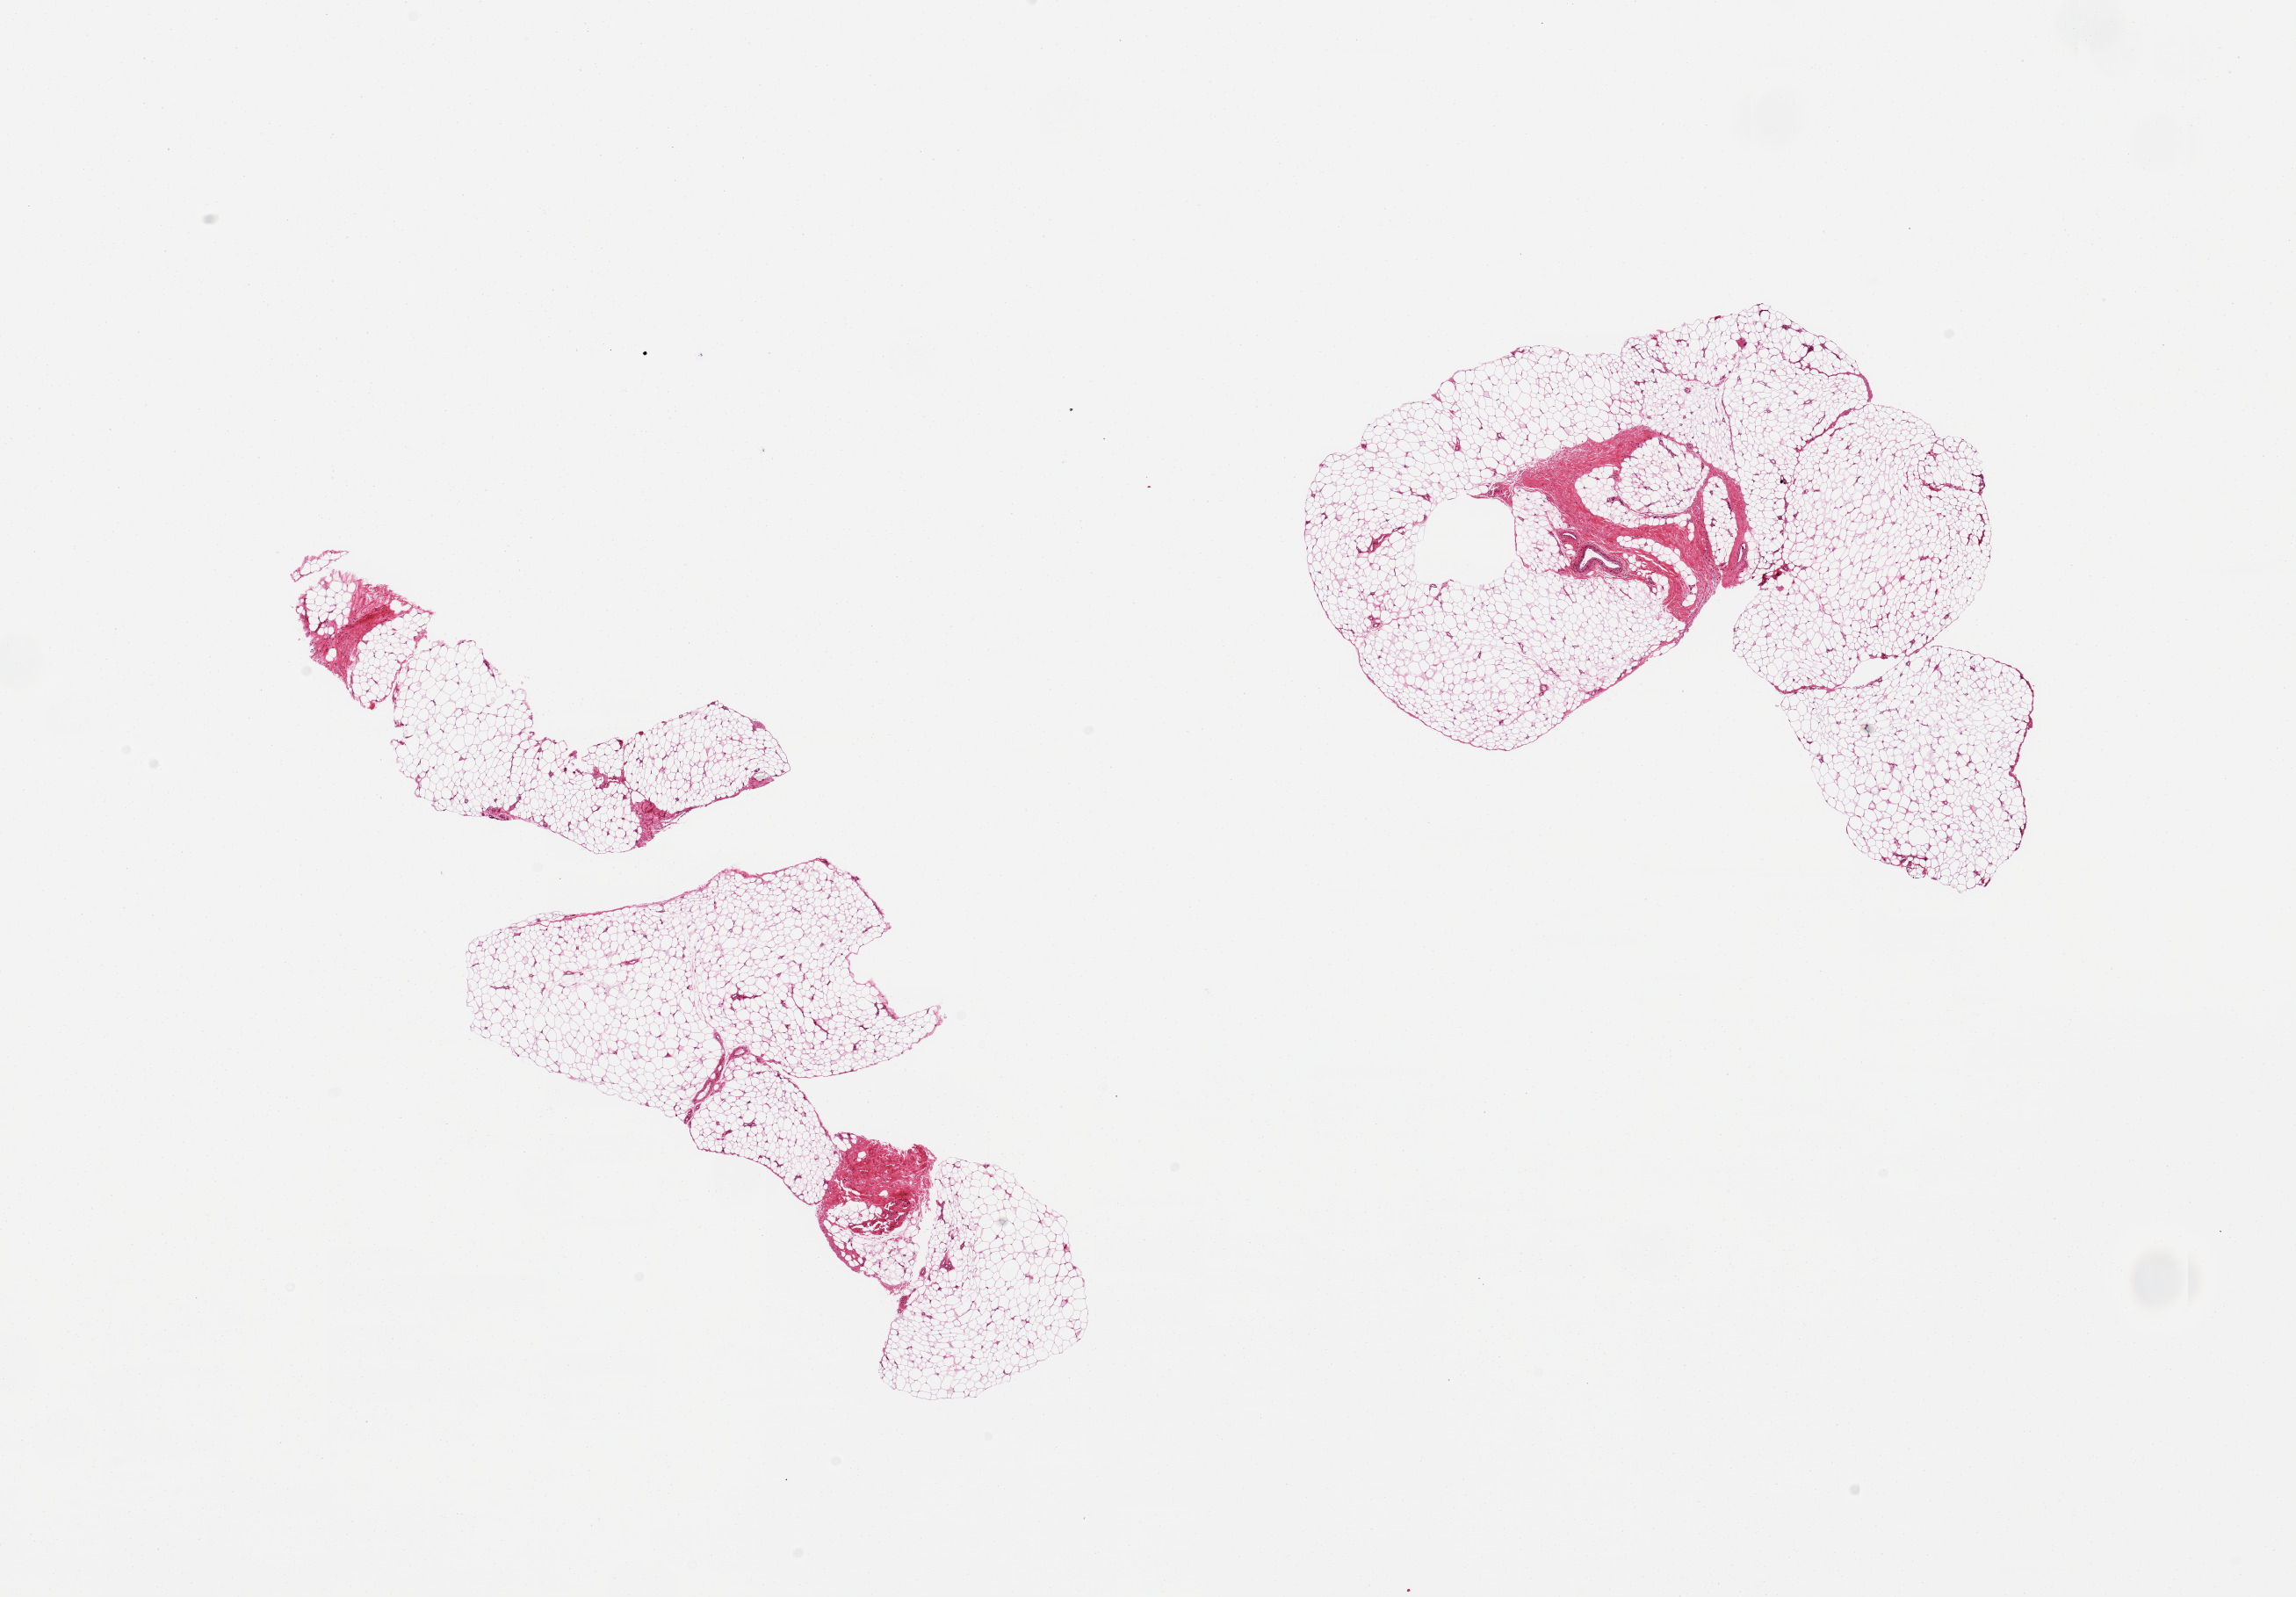
H&E whole-slide image, a low-resolution overview of the entire scanned area, about 20.7 x 14.4 mm. PAXgene-fixed paraffin-embedded (PFPE) section. Sampled site (target tissue): adipose tissue. Donor tissue sample. Donor: female.
- pathologist's review note for this sample: 2 pieces; 10% fibrous content